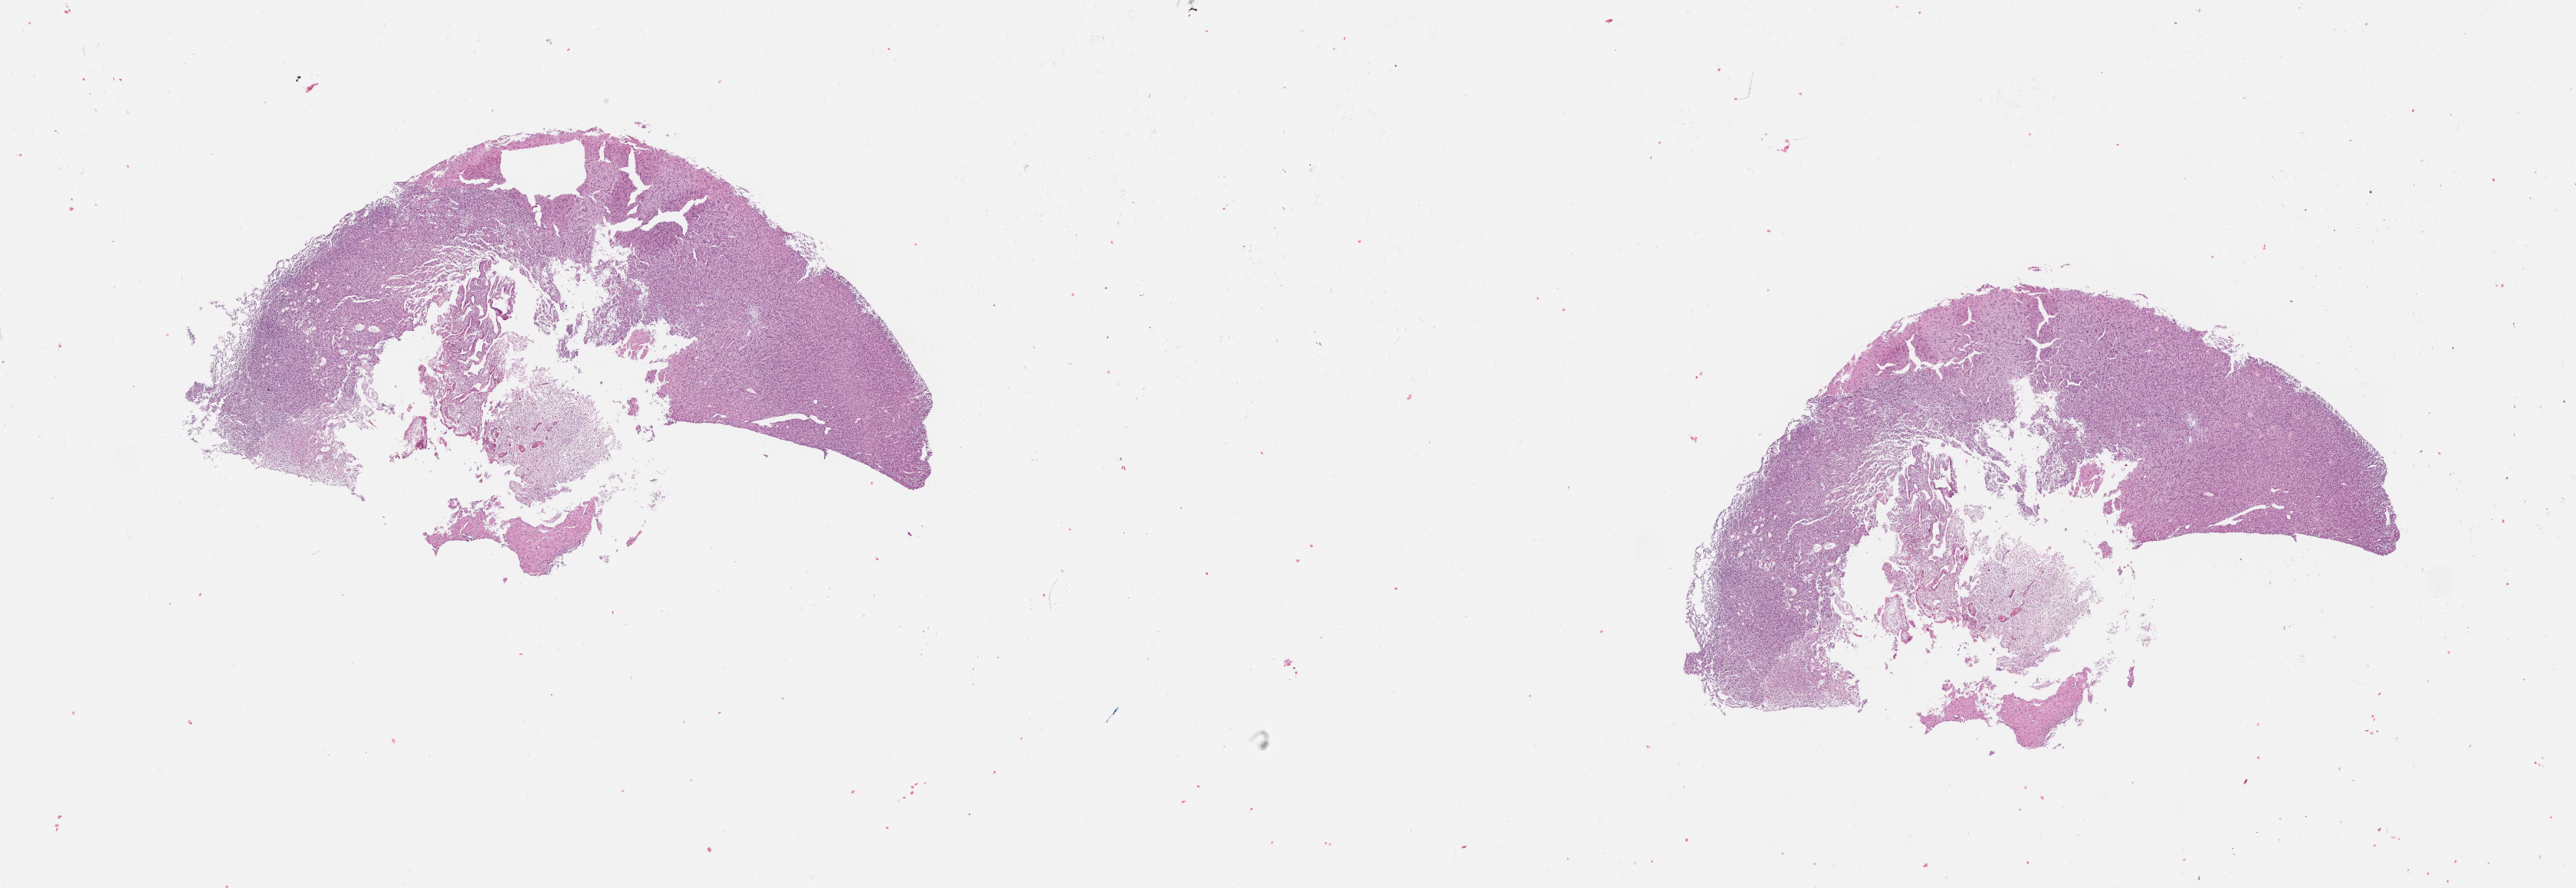
Whole-slide histology image, H&E — low-resolution overview of the scanned area, about 27.1 x 9.3 mm, brain, tumour tissue. 80-year-old female patient.
• diagnosis: Glioblastoma
• primary tumour site (as recorded): frontal lobe